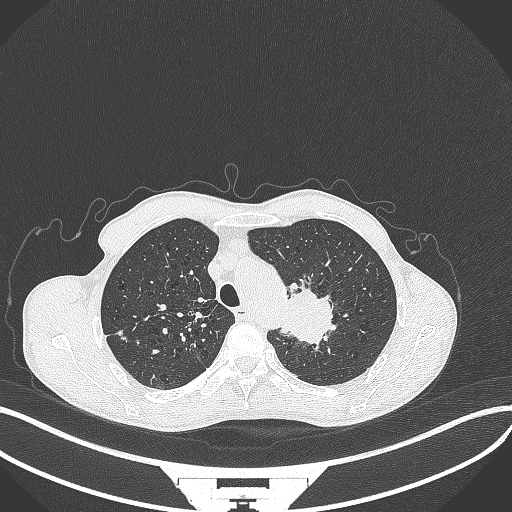
Chest CT, one axial slice; position 328 of 386 along the scan axis; reconstruction kernel B70f; lung window (W 1500 / L -600 HU); 512 × 512 image matrix, field of view 400 × 400 mm. Male patient, age 65 years. From the clinical record (not read from this slice): clinical TNM (as recorded): T2b N0 M0; histopathological grade: G2.
Structures marked on this image (rectangle marked by the reading radiologist):
- lung tumour (recorded histology: adenocarcinoma): box from (x=273, y=282) to (x=336, y=348) px